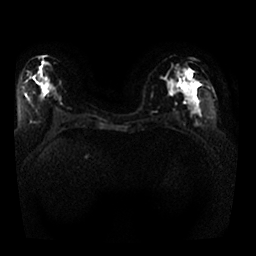
Breast MRI, one axial slice. Position 12 of 25 along the scan axis. Diffusion-weighted series; image 2 of 4 stored at this slice position (different b-values; order by instance number). 1.5 T. 256 × 256 image matrix, field of view 350 × 350 mm. Female patient.
Annotated regions visible in this slice (expert manual segmentation):
- tumour on diffusion-weighted imaging: bounding box [x1, y1, x2, y2] px = [178, 79, 186, 91]